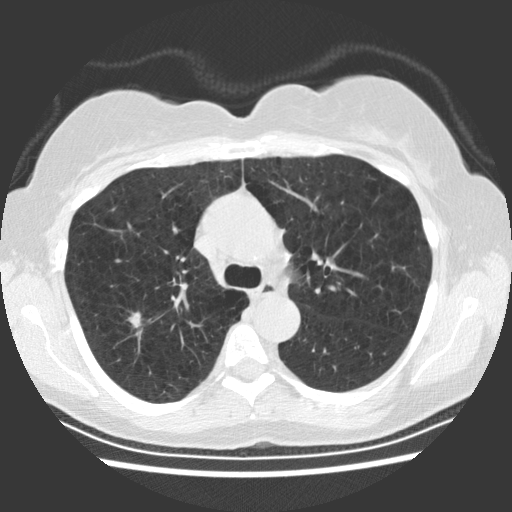
Low-dose screening chest CT, one axial slice. Position 161 of 234 along the scan axis. 120 kVp. Lung window (W 1500 / L -600 HU). 512 × 512 image matrix.
Outlined on this slice (outlined manually by an expert reader):
- lesion 1 (tumor, upper lobe of right lung): bounding box <128,312,141,328> (left, top, right, bottom; pixels)